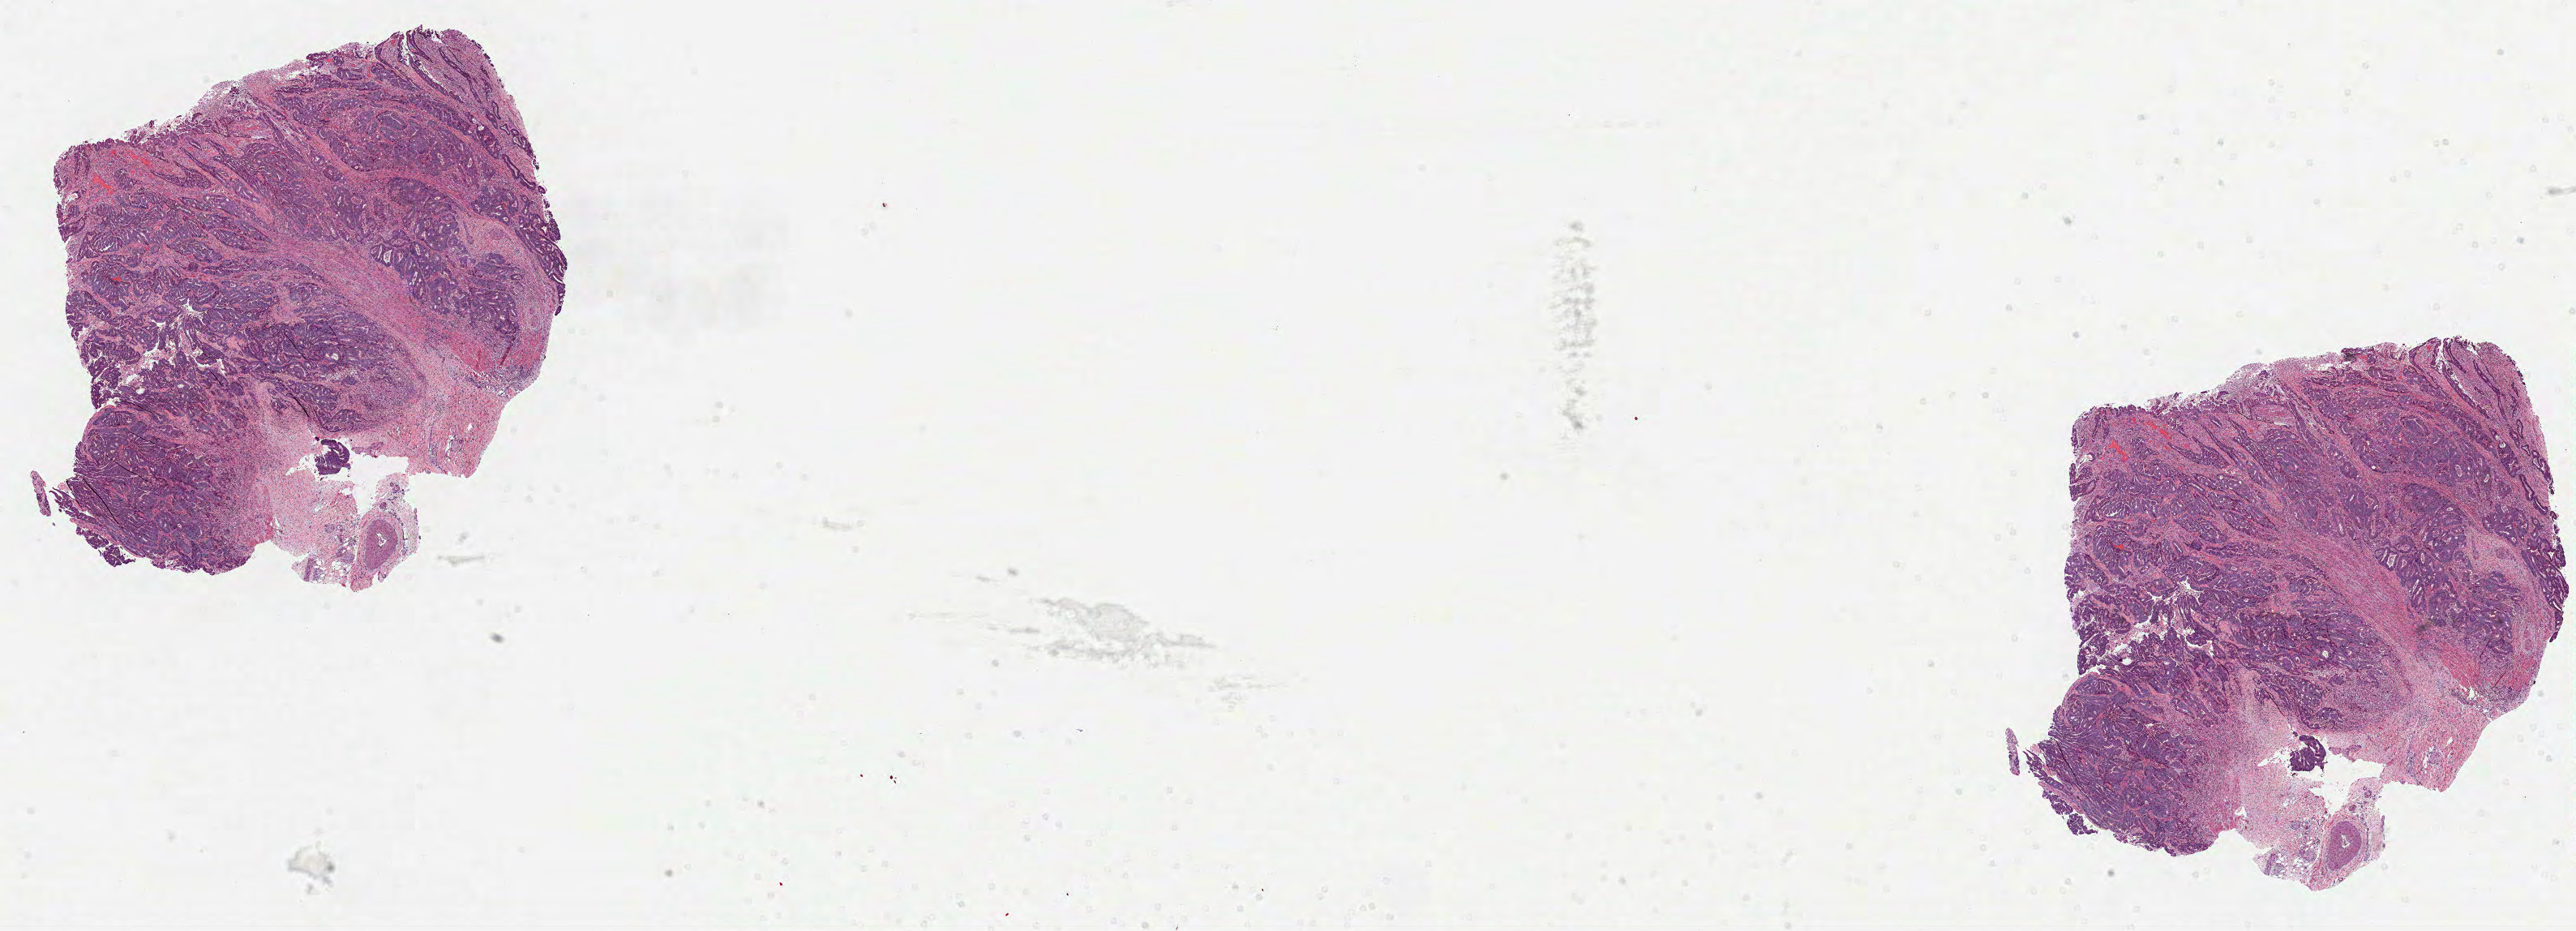
H&E-stained whole-slide image — shown as a low-resolution overview of the whole scanned area (about 25.6 x 9.3 mm, acquisition: 40x scan); formalin-fixed paraffin-embedded (FFPE) diagnostic section; colon, primary tumour sample. Male, age 85 years at initial diagnosis.
- AJCC pathologic stage: IV (6th edition)
- pathologic diagnosis: Adenocarcinoma, NOS
- TNM: T3 N2 M1